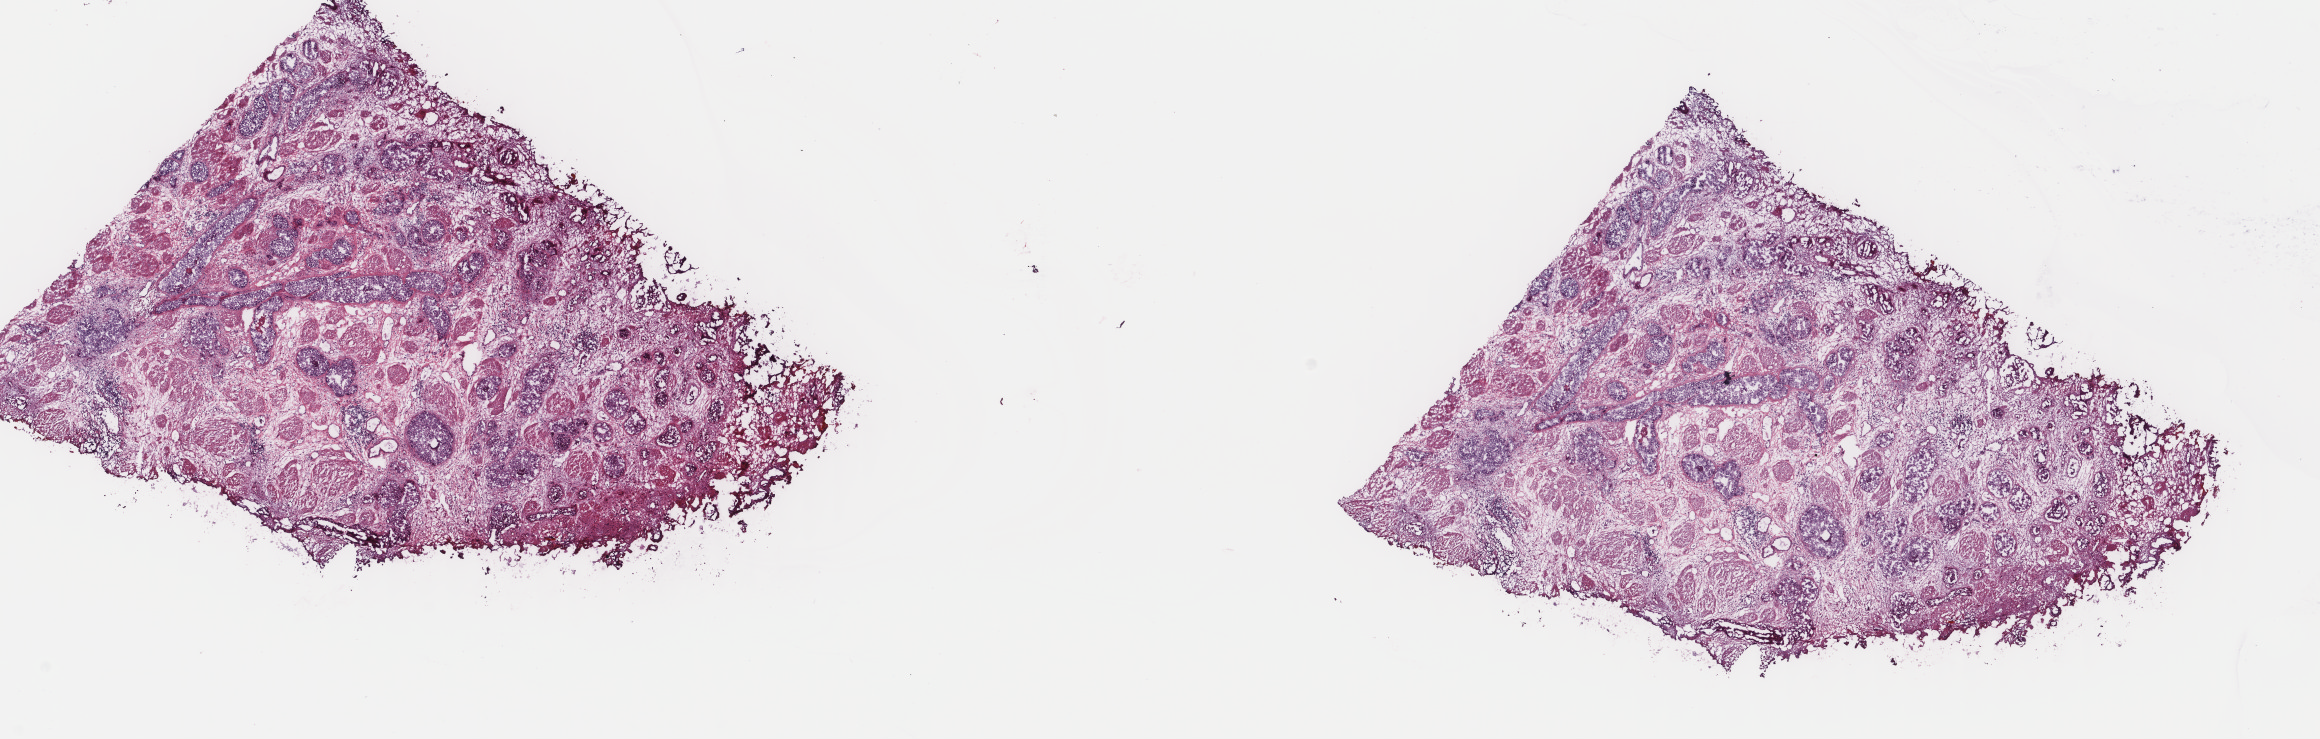
H&E-stained whole-slide image, shown as a low-resolution overview of the whole scanned area (about 18.4 x 5.9 mm, from a 40x scan). Frozen section from the top of the tissue portion. Primary tumour sample from the bladder. Male, age 57 years at initial diagnosis. Histologic grade: high grade. Pathologist review of this section (percent, as recorded): tumour cells 70%, tumour nuclei 70%, normal cells 0%, stromal cells 30%, necrosis 0%. Infiltration values recorded for this section: lymphocyte infiltration 2%, monocyte infiltration 0%, neutrophil infiltration 0%.
* AJCC pathologic stage: II (7th edition)
* histologic diagnosis: Transitional cell carcinoma